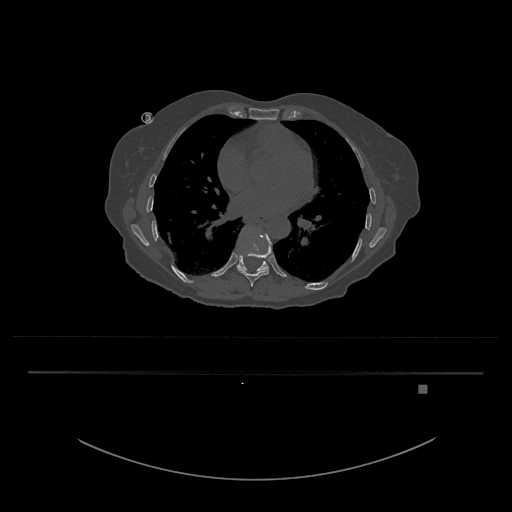
CT including the spine, one axial slice. Position 743 of 797 along the scan axis. Reconstruction kernel Br40s/3. Bone window (W 1800 / L 400 HU). 0.5 mm slice thickness. 512 × 512 image matrix, field of view 500 × 500 mm. Patient: female, 57 years. Case-level facts recorded for this patient, not image findings: primary cancer: cervical.
Annotated regions visible in this slice (semi-automatic segmentation, software-assisted and operator-edited):
- T10 vertebra: bounding box [x1, y1, x2, y2] px = [237, 228, 269, 272]
- T9 vertebra: [238, 235, 271, 287]